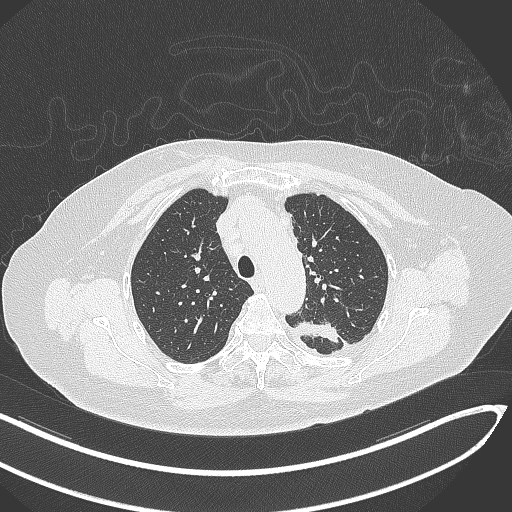
Chest CT, one axial slice; position 237 of 270 along the scan axis; reconstruction kernel B70f; 120 kVp; lung window (W 1500 / L -600 HU); 1 mm slice thickness; 512 × 512 image matrix. Female patient, age 76 years. From the clinical record (not read from this slice): clinical TNM (as recorded): T1c N0 M0.
Outlined on this slice (rectangle marked by the reading radiologist):
- lung tumour (recorded histology: adenocarcinoma): bounding box [x1, y1, x2, y2] px = [287, 319, 339, 347]